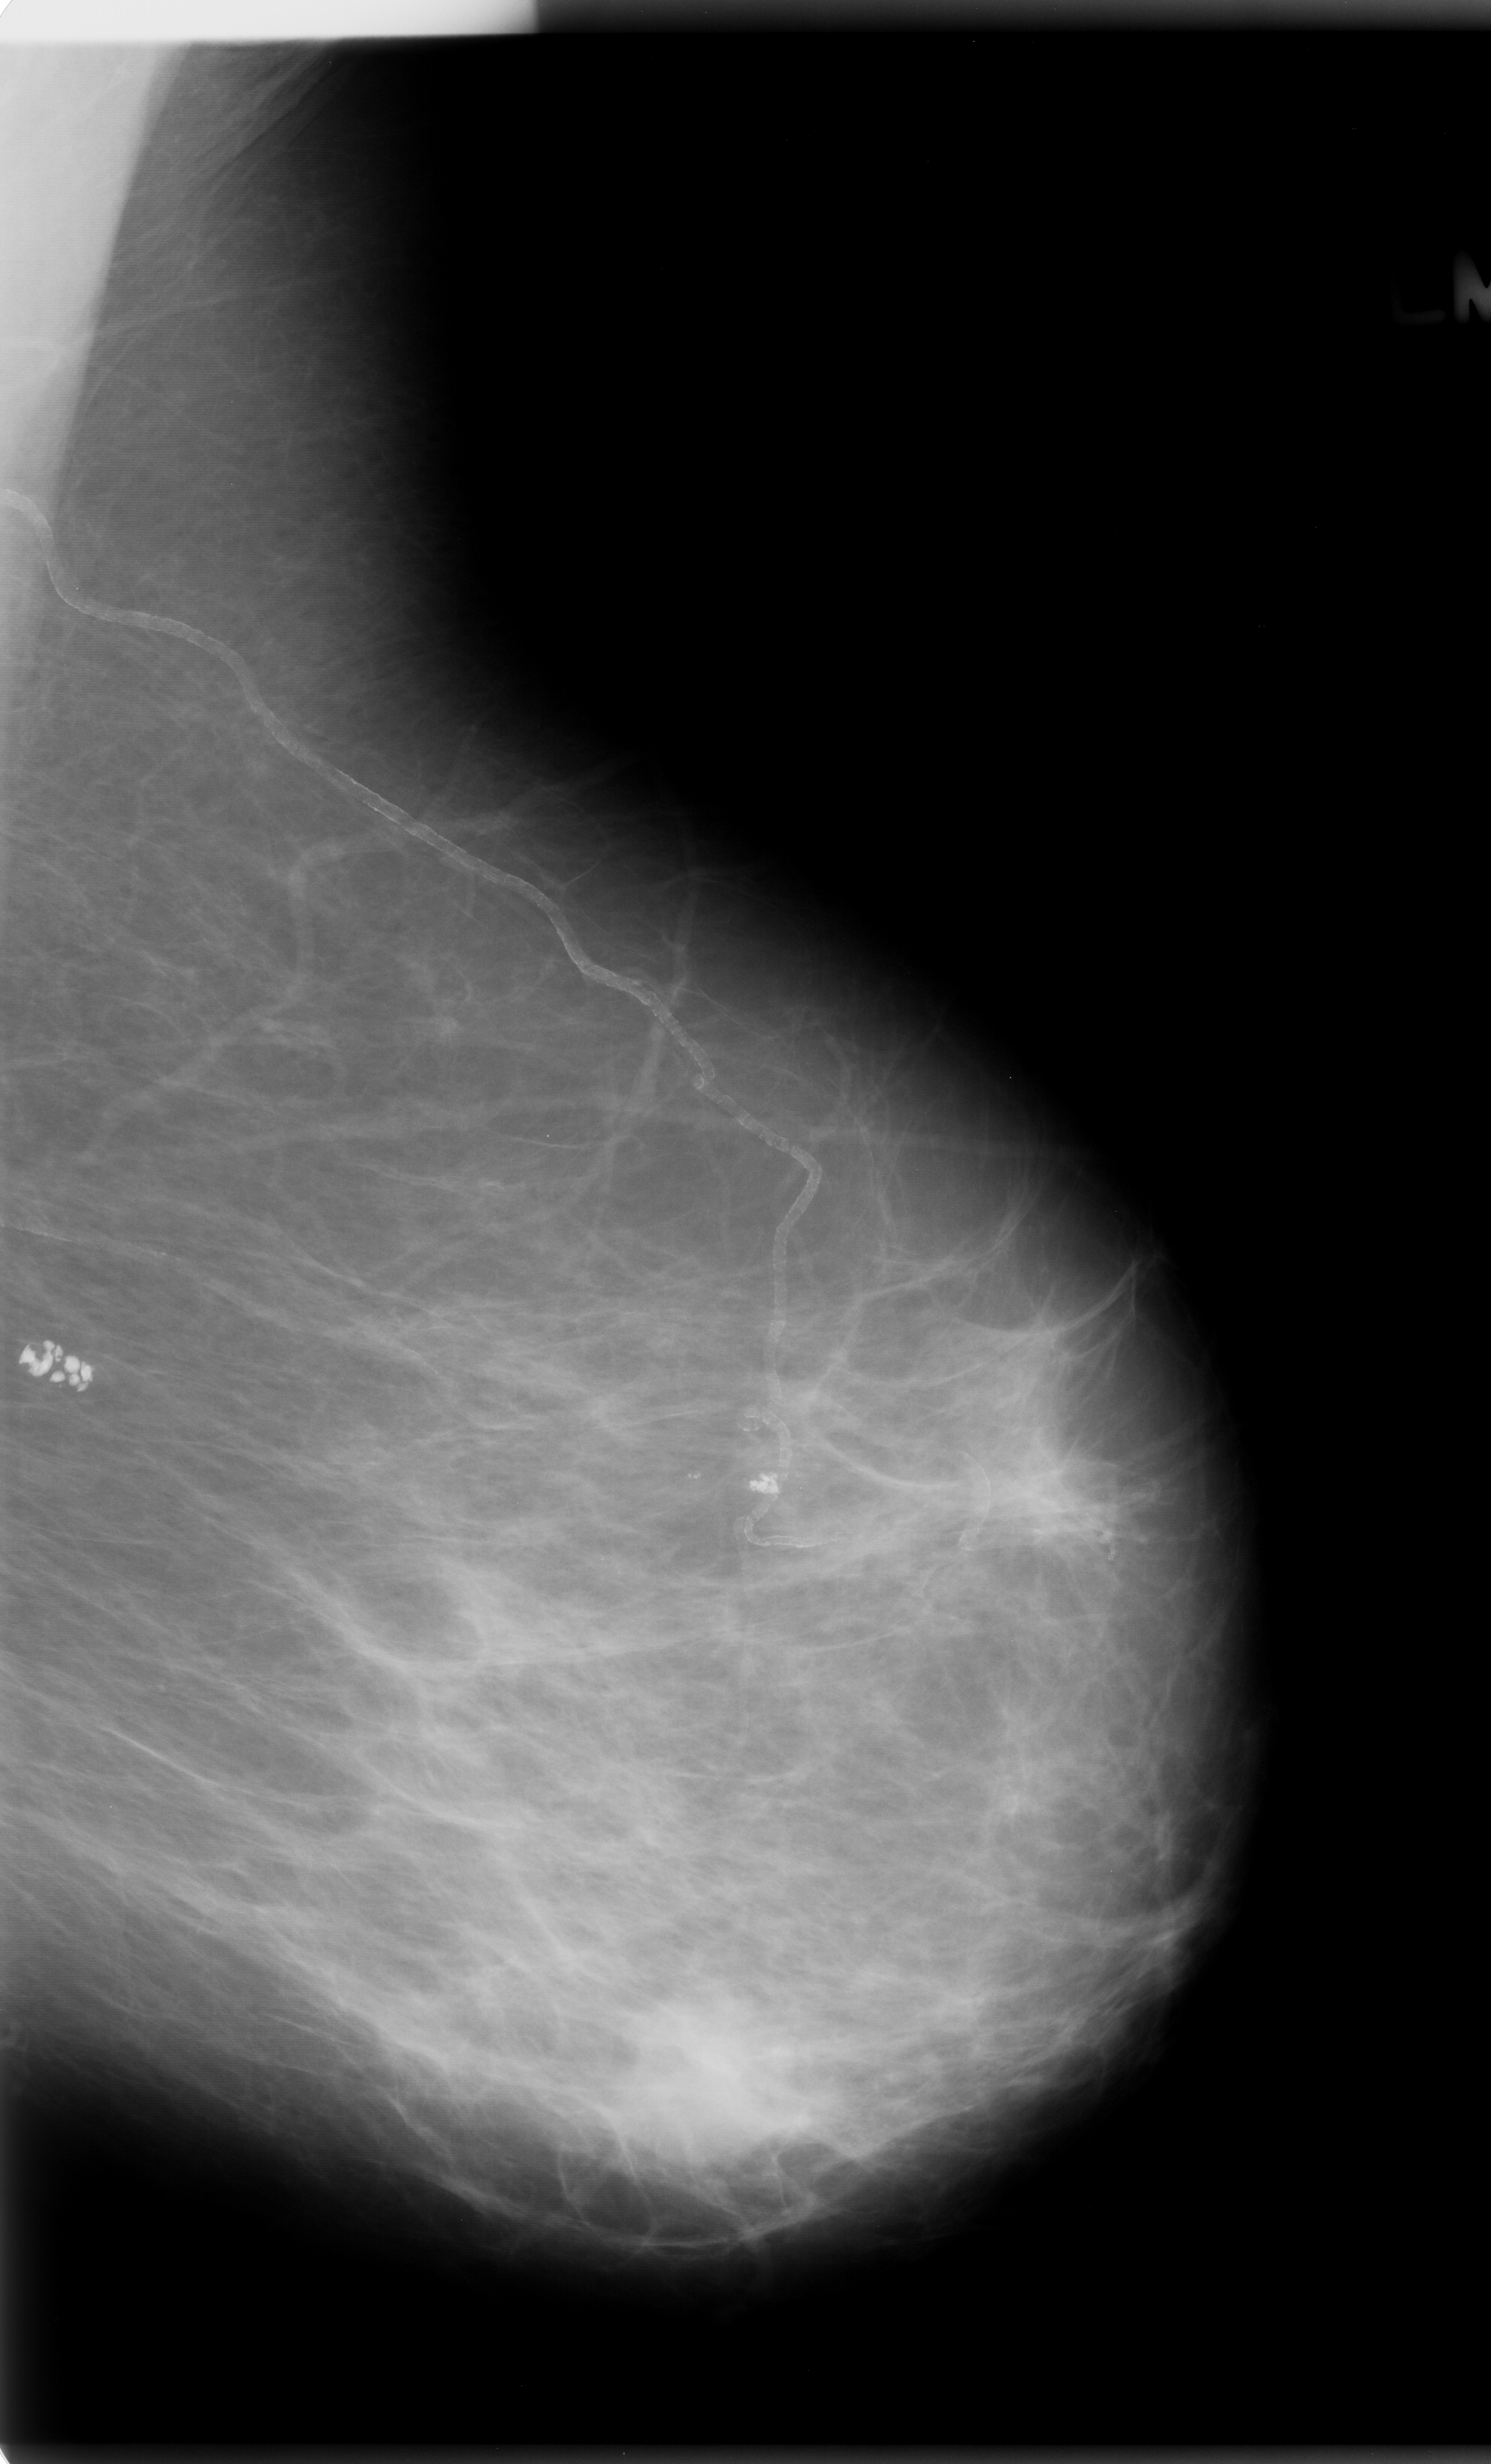
Mammogram (digitized film), left breast, mediolateral oblique (MLO) view.
- Marked findings (only marked abnormalities are described; nothing is implied about the rest of the image): mass, shape lobulated, margins microlobulated; BI-RADS assessment category 5; pathology result (as recorded, not read from the image): malignant.